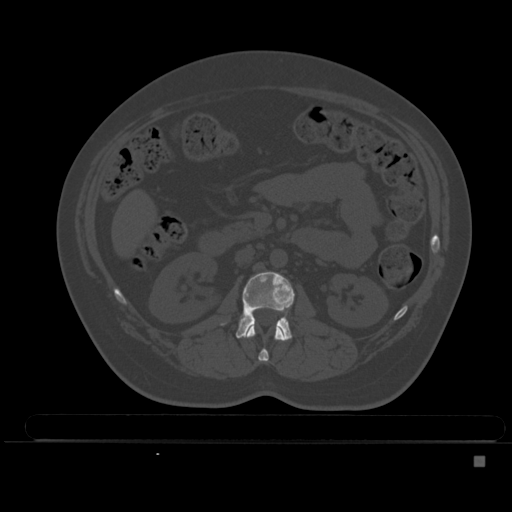
CT including the spine, one axial slice; position 181 of 495 along the scan axis; bone window (W 1800 / L 400 HU); 1.5 mm slice thickness; 512 × 512 image matrix, field of view 404 × 404 mm. Female patient, age 33 years. From the clinical record (not read from this slice): primary cancer: breast.
Outlined on this slice (semi-automatic segmentation, software-assisted and operator-edited):
- L1 vertebra: box from (x=242, y=325) to (x=286, y=362) px
- L2 vertebra: (x=222, y=271)–(x=295, y=340)